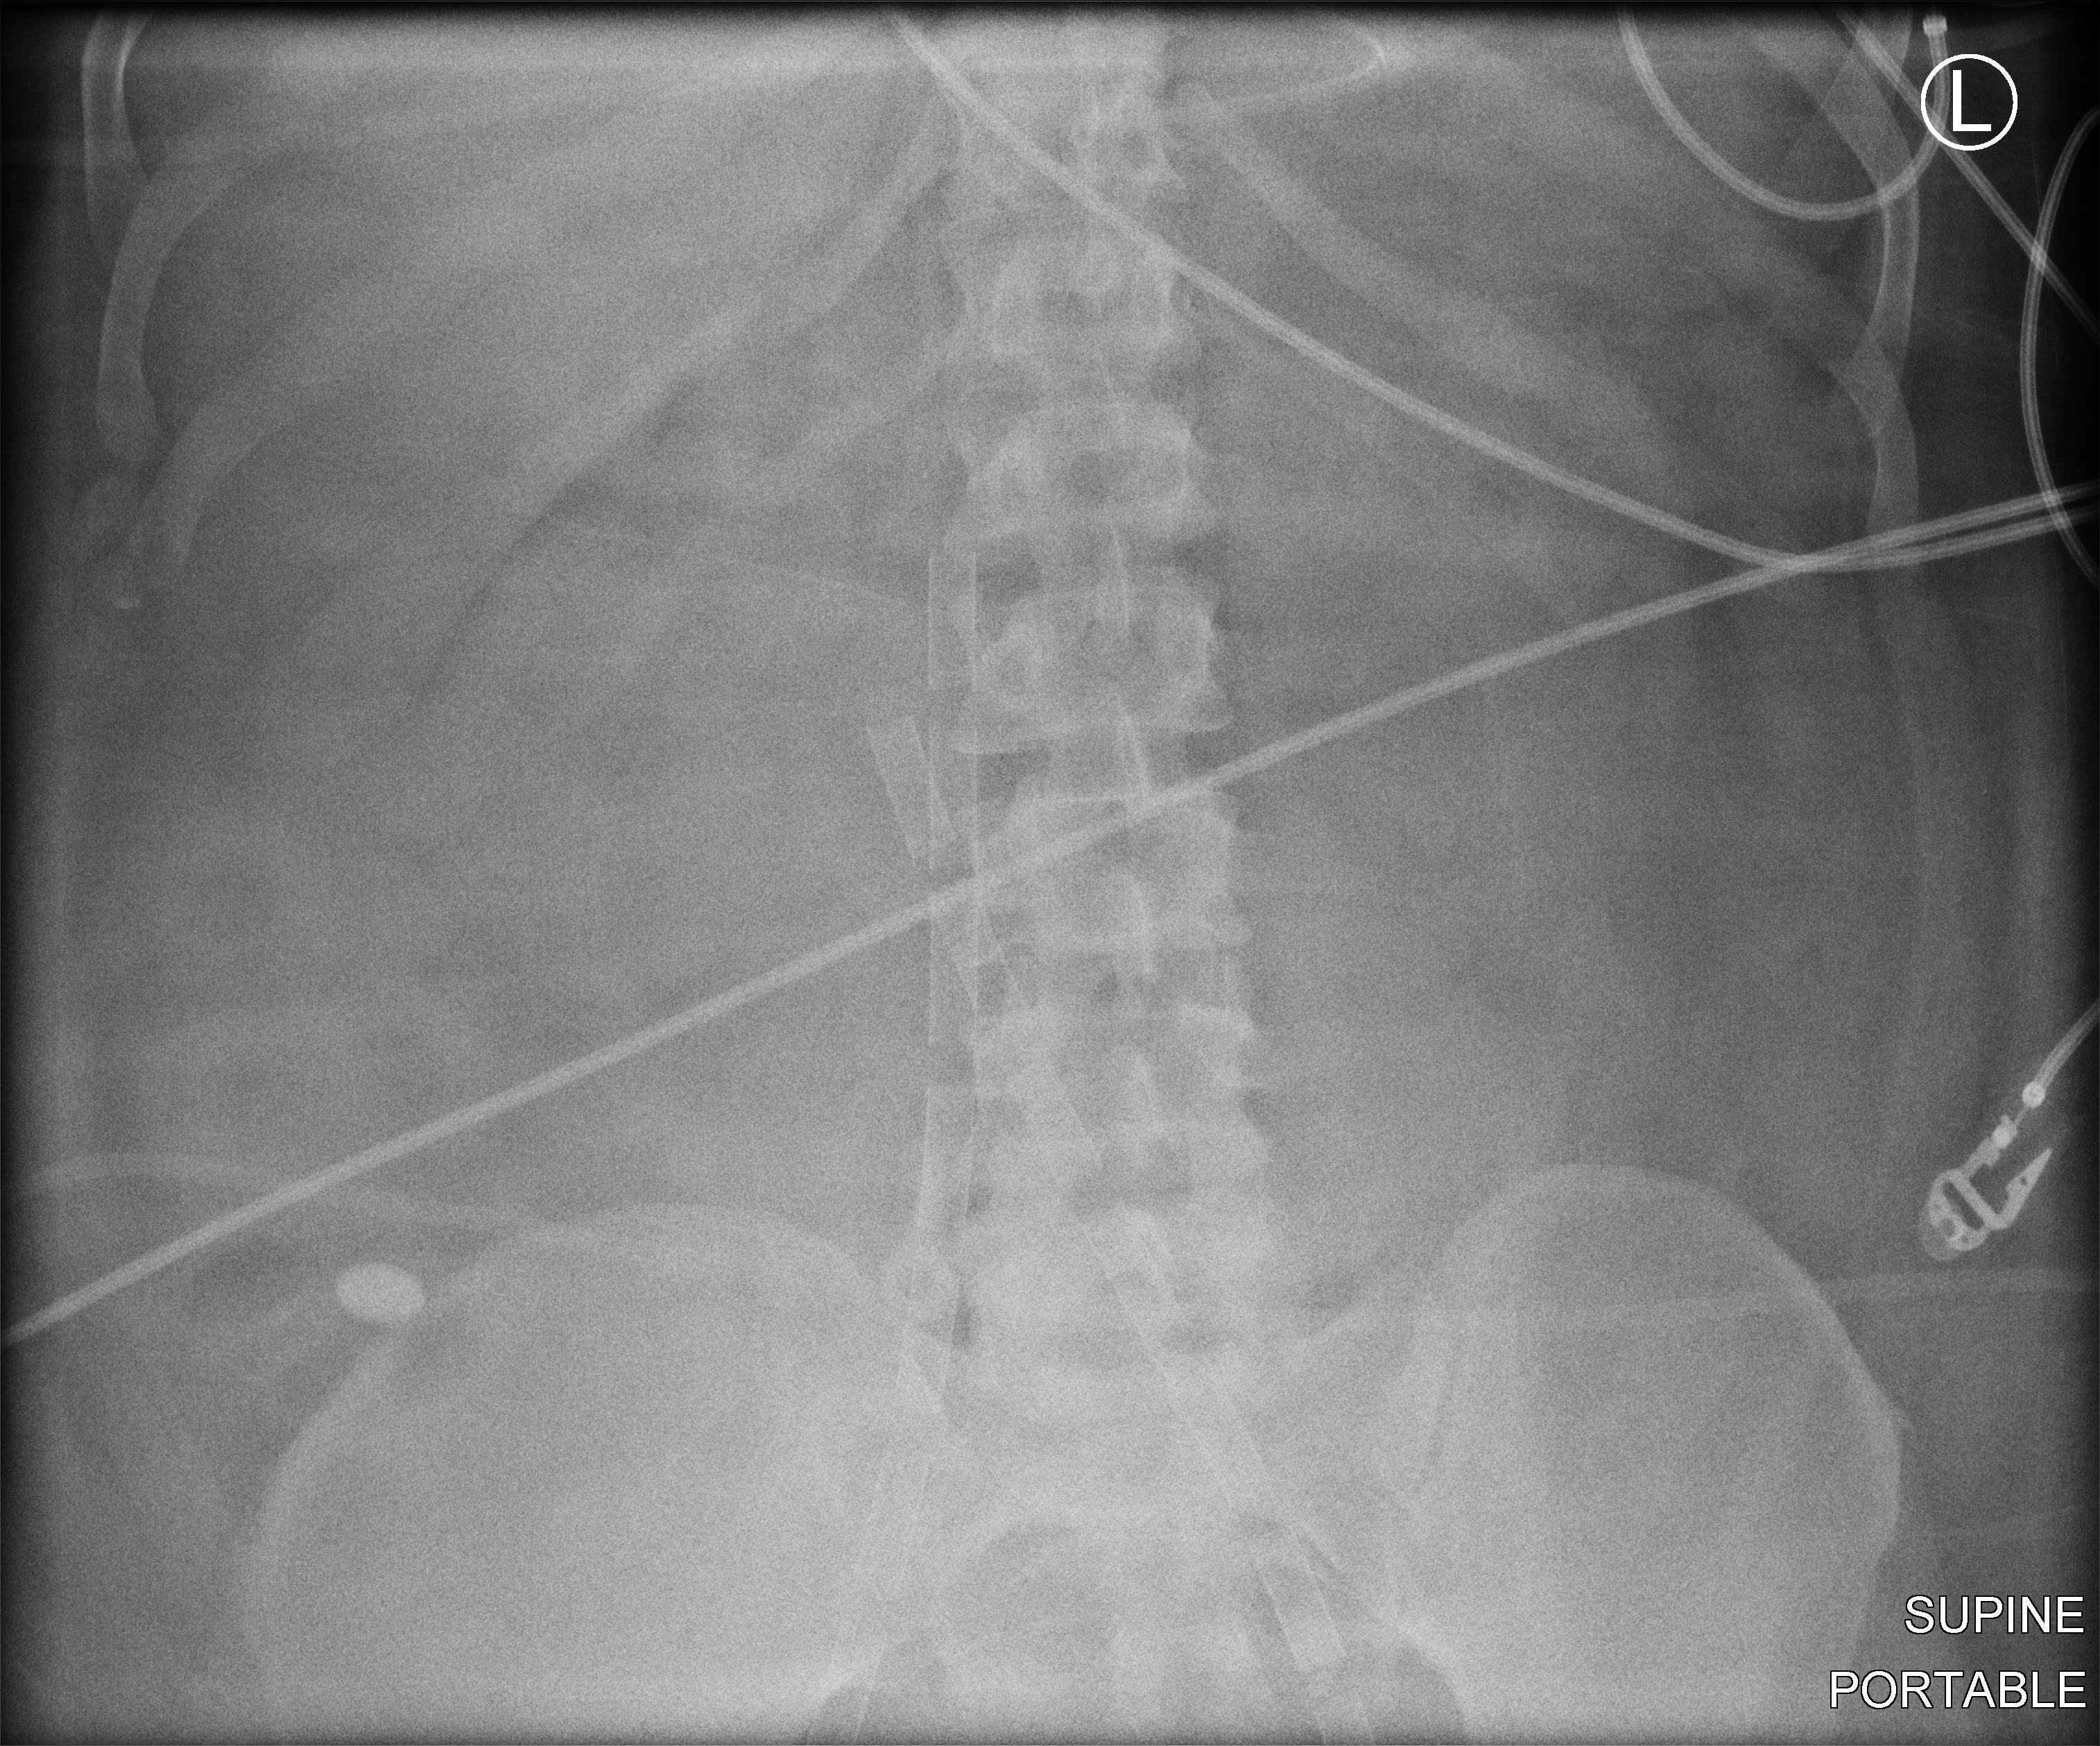
Bedside abdomen radiograph (computed radiography). Adult patient hospitalised with COVID-19, age 18–59 years.
From the hospital-stay record, not from the radiograph (when in the stay this image was taken is not recorded): smoking status (admission record): never.